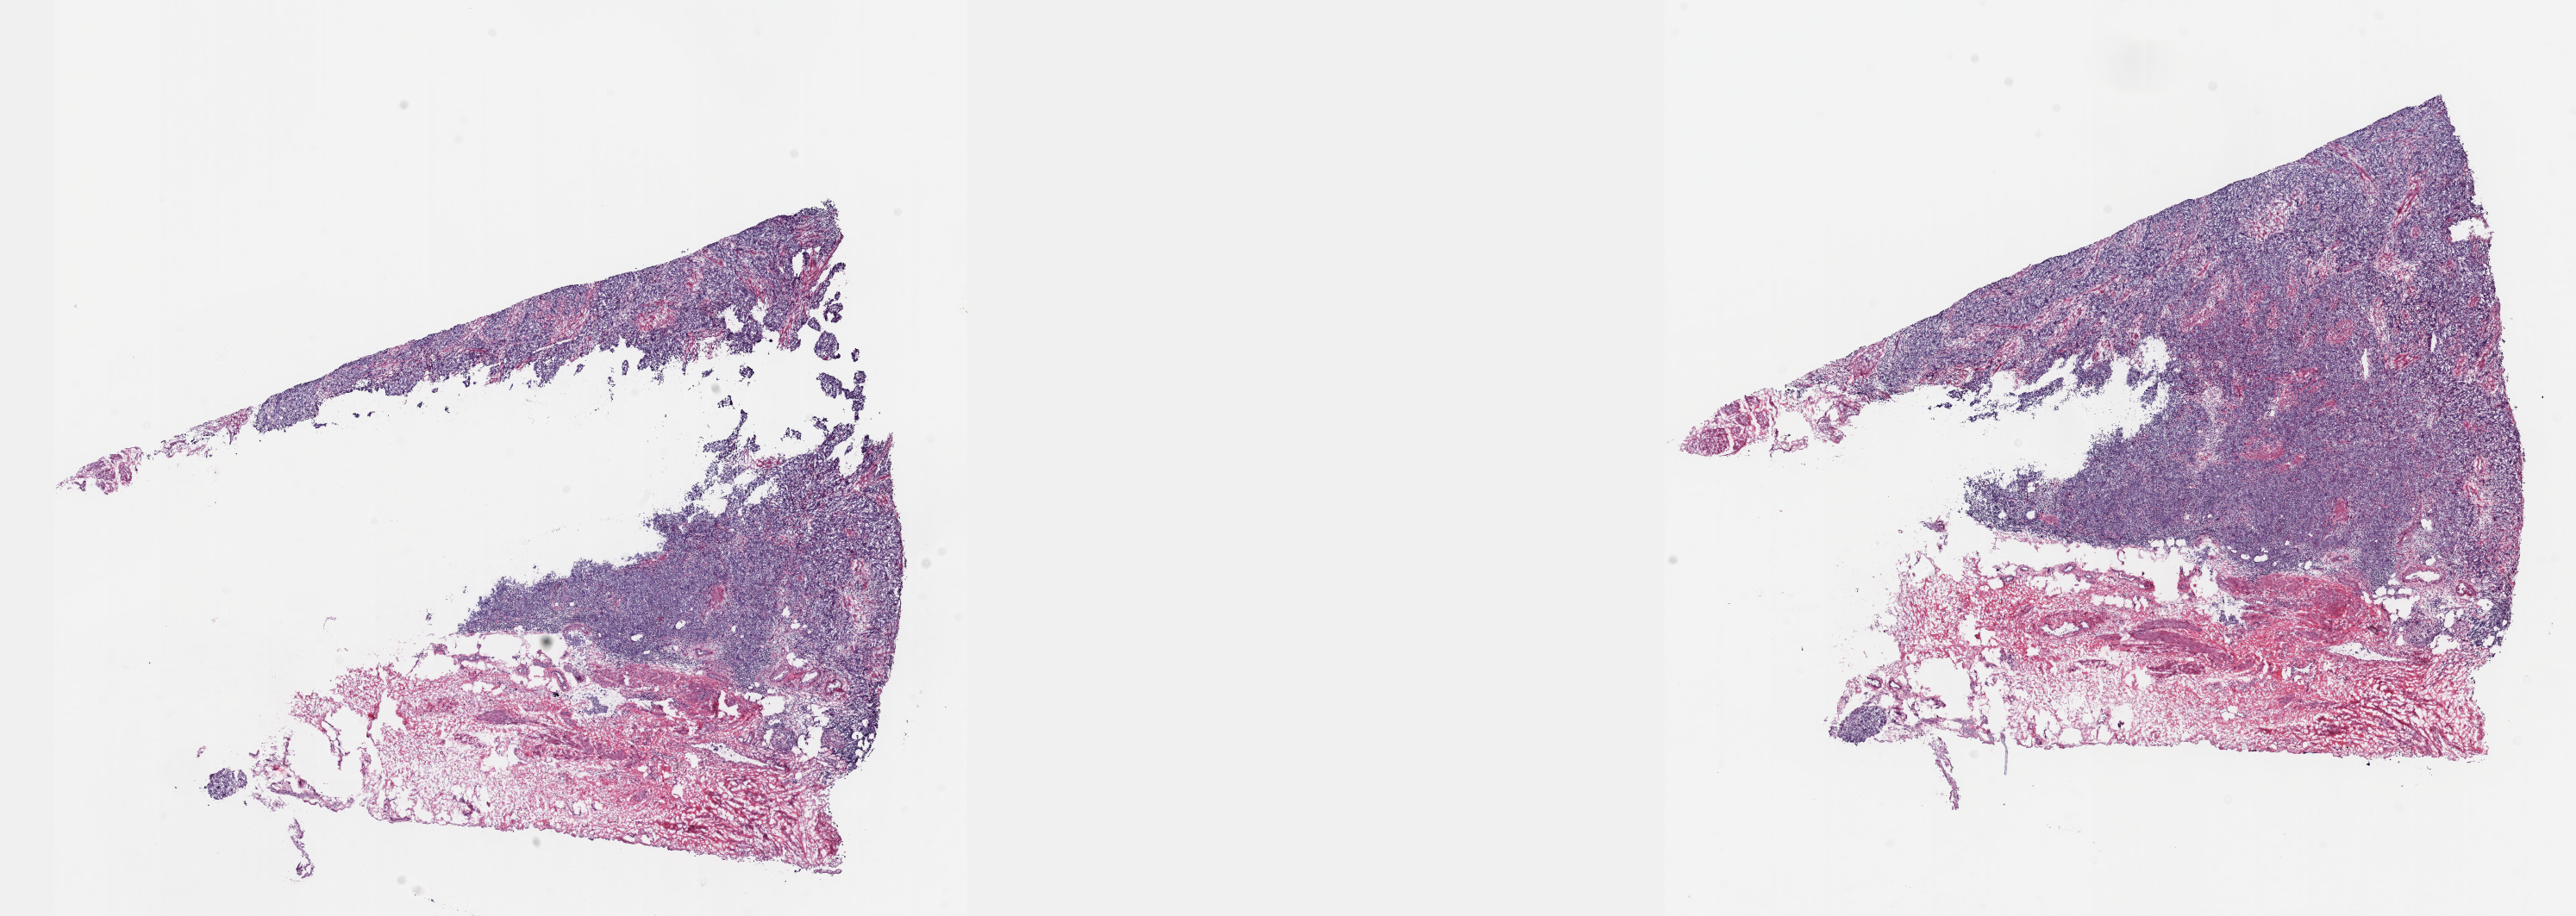
Whole-slide histology image, H&E, a low-resolution overview of the entire scanned area, about 24.1 x 8.6 mm, frozen section, bladder, primary tumour sample. Female patient; age at initial diagnosis 73 years. Histologic grade: high grade. Slide review estimates, as recorded: tumour cells 80%, tumour nuclei 80%, normal cells 0%, stromal cells 20%, necrosis 0%. Infiltration values recorded for this section: lymphocyte infiltration 2%, monocyte infiltration 1%, neutrophil infiltration 4%.
- histologic diagnosis: Papillary transitional cell carcinoma
- AJCC pathologic stage: II